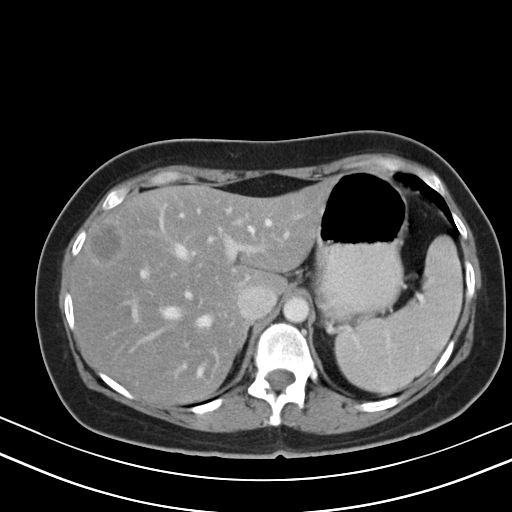
Contrast-enhanced abdominal CT, one axial slice. Position 35 of 47 along the scan axis. Reconstruction kernel B40s. 130 kVp. Intravenous contrast given. Soft-tissue window (W 400 / L 40 HU). 512 × 512 image matrix. Female patient. From the clinical record (not read from this slice): diagnosis: colorectal cancer liver metastases, imaged before liver resection; multiple liver metastases: no; largest metastasis: 3.5 cm; disease in both lobes: no.
Annotated regions visible in this slice (expert manual segmentation):
- hepatic veins: box from (x=138, y=206) to (x=271, y=377) px
- liver: (x=72, y=185)–(x=327, y=401)
- planned liver remnant (the part of the liver to remain after resection): (x=72, y=186)–(x=327, y=401)
- portal vein (with intrahepatic branches): (x=123, y=214)–(x=289, y=325)
- liver metastasis: (x=91, y=226)–(x=122, y=263)